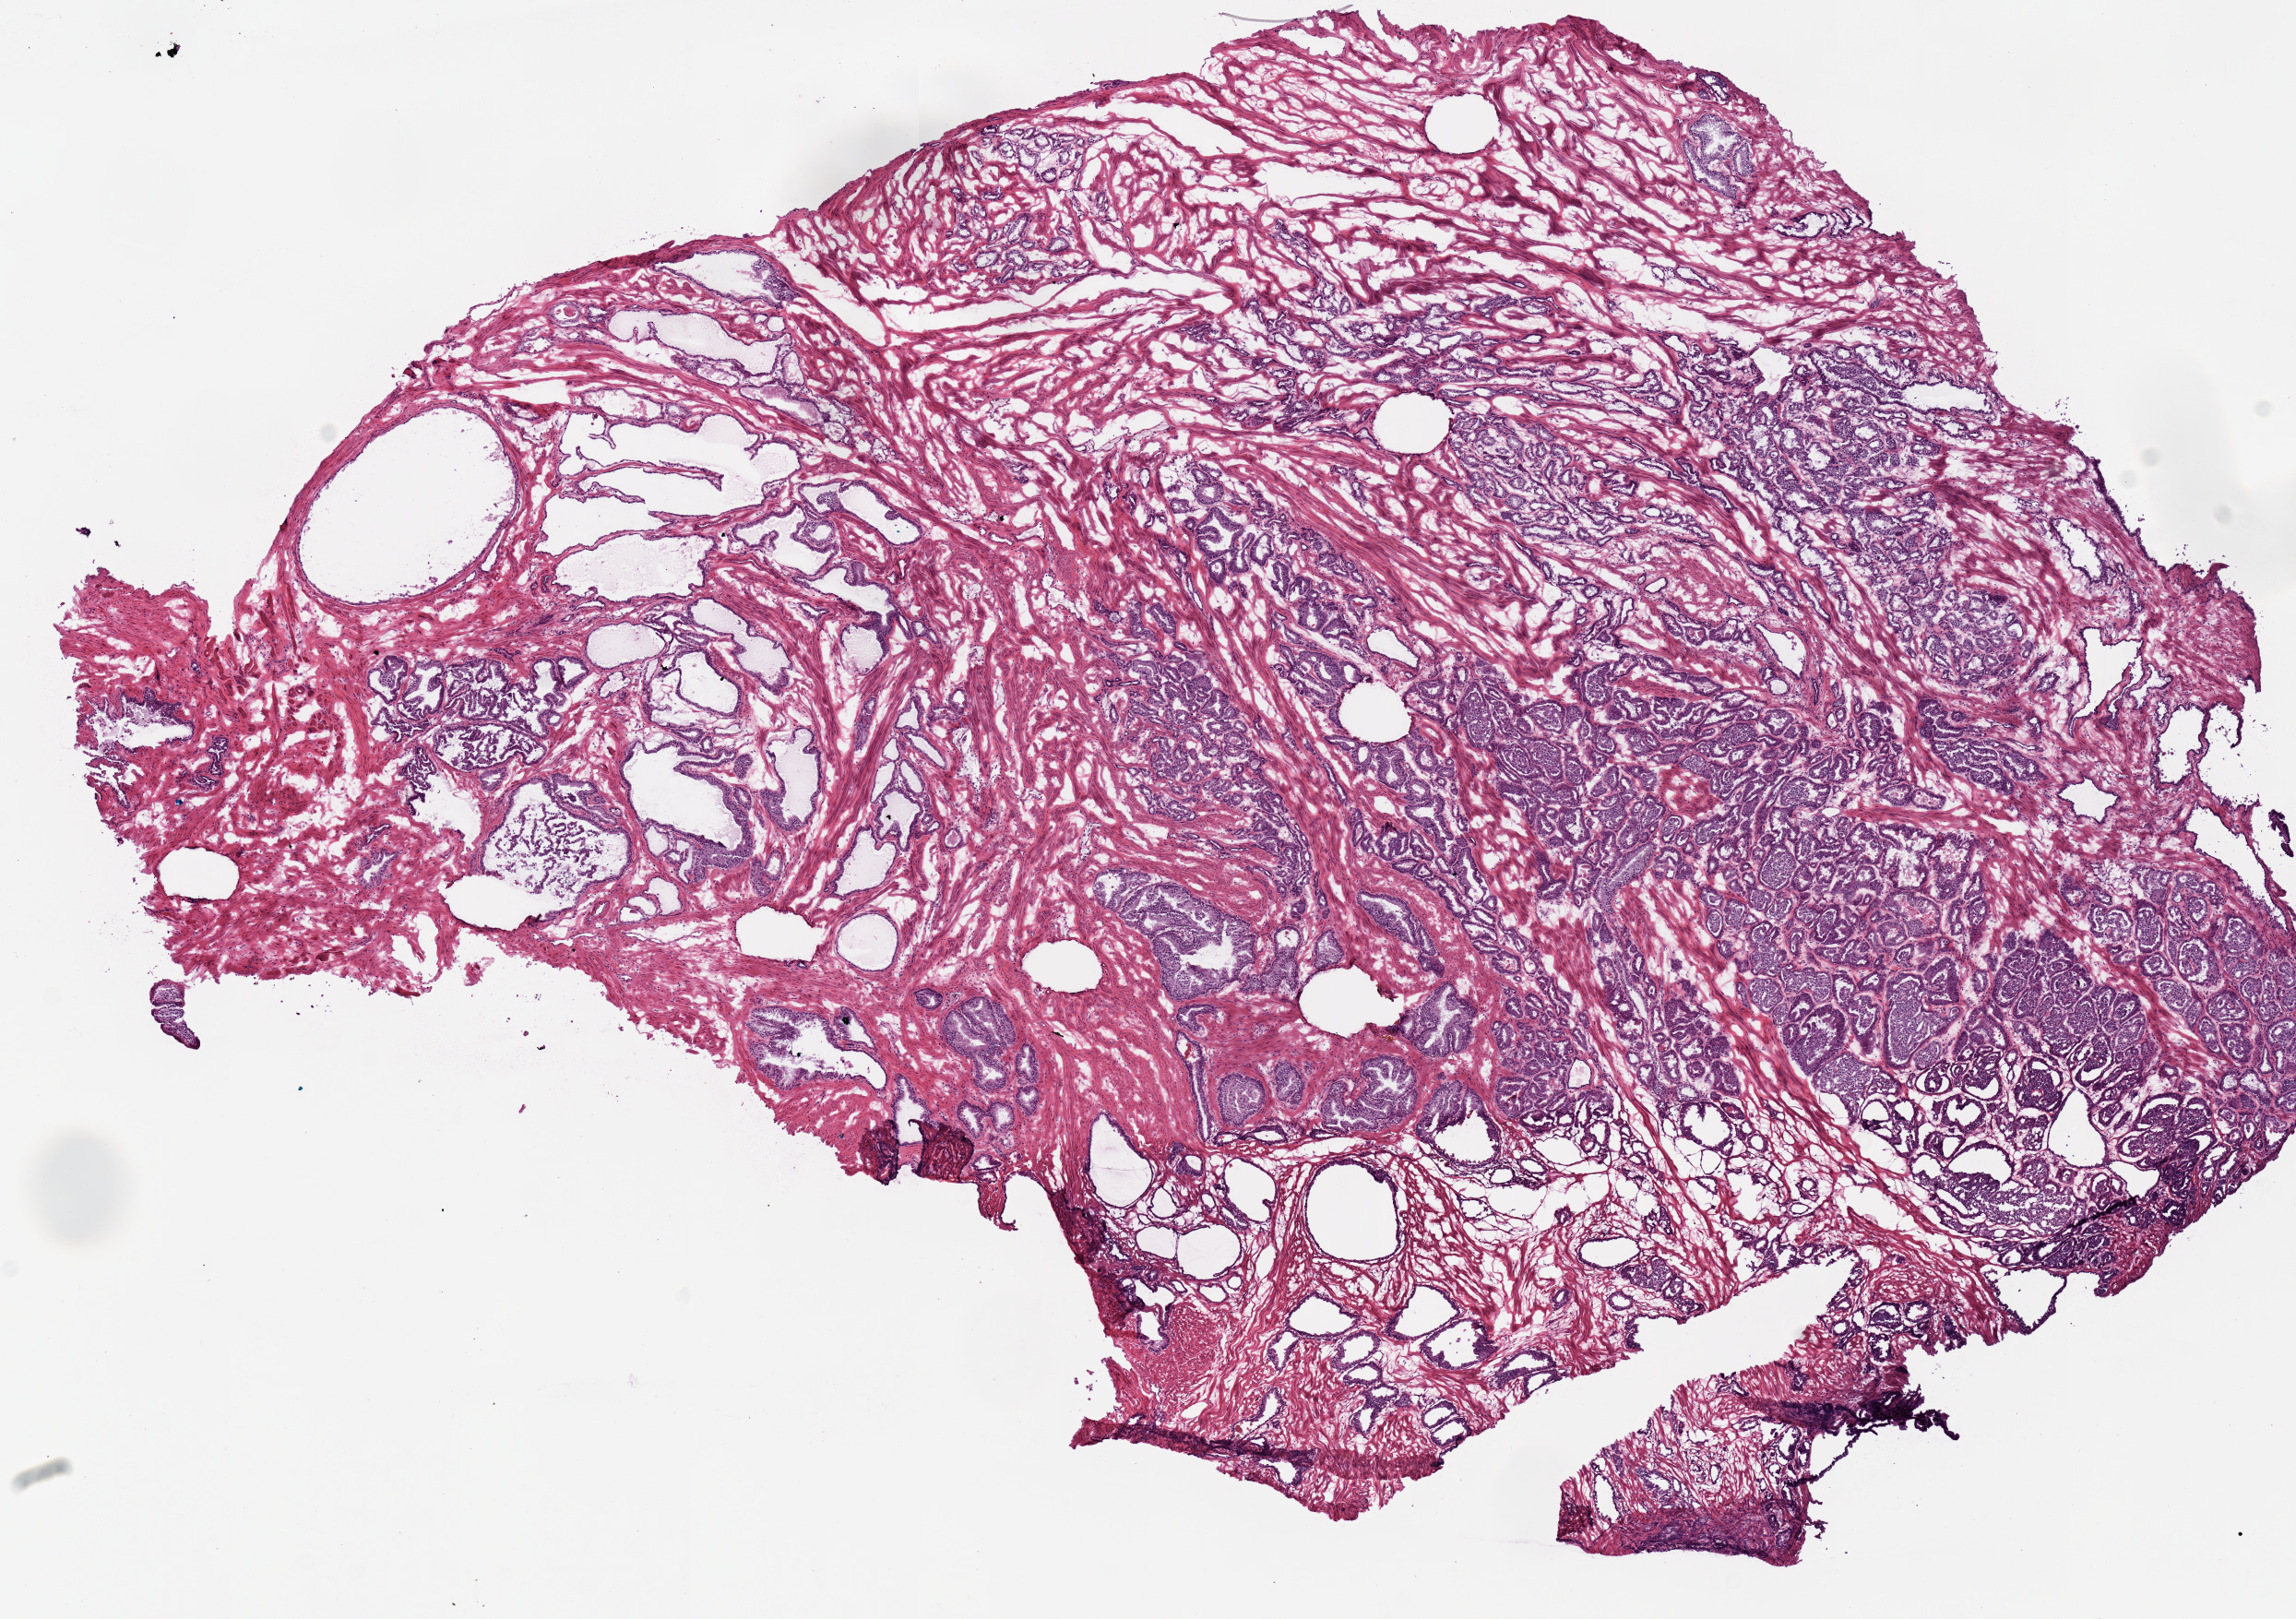
Digitized H&E-stained tissue section (whole slide) — shown as a low-resolution overview of the whole scanned area (about 9.8 x 6.9 mm); frozen section; primary tumour sample from the prostate. Patient: male, age at initial diagnosis 71 years. Gleason score: 7 (3+4). Pathologist review of this section (percent, as recorded): tumour cells 70%, tumour nuclei 70%, normal cells 10%, stromal cells 20%, necrosis 0%.
Laterality: bilateral. Lymph nodes positive (case pathology): 0 of 40 examined. Diagnosis: Acinar cell carcinoma (prostate gland).